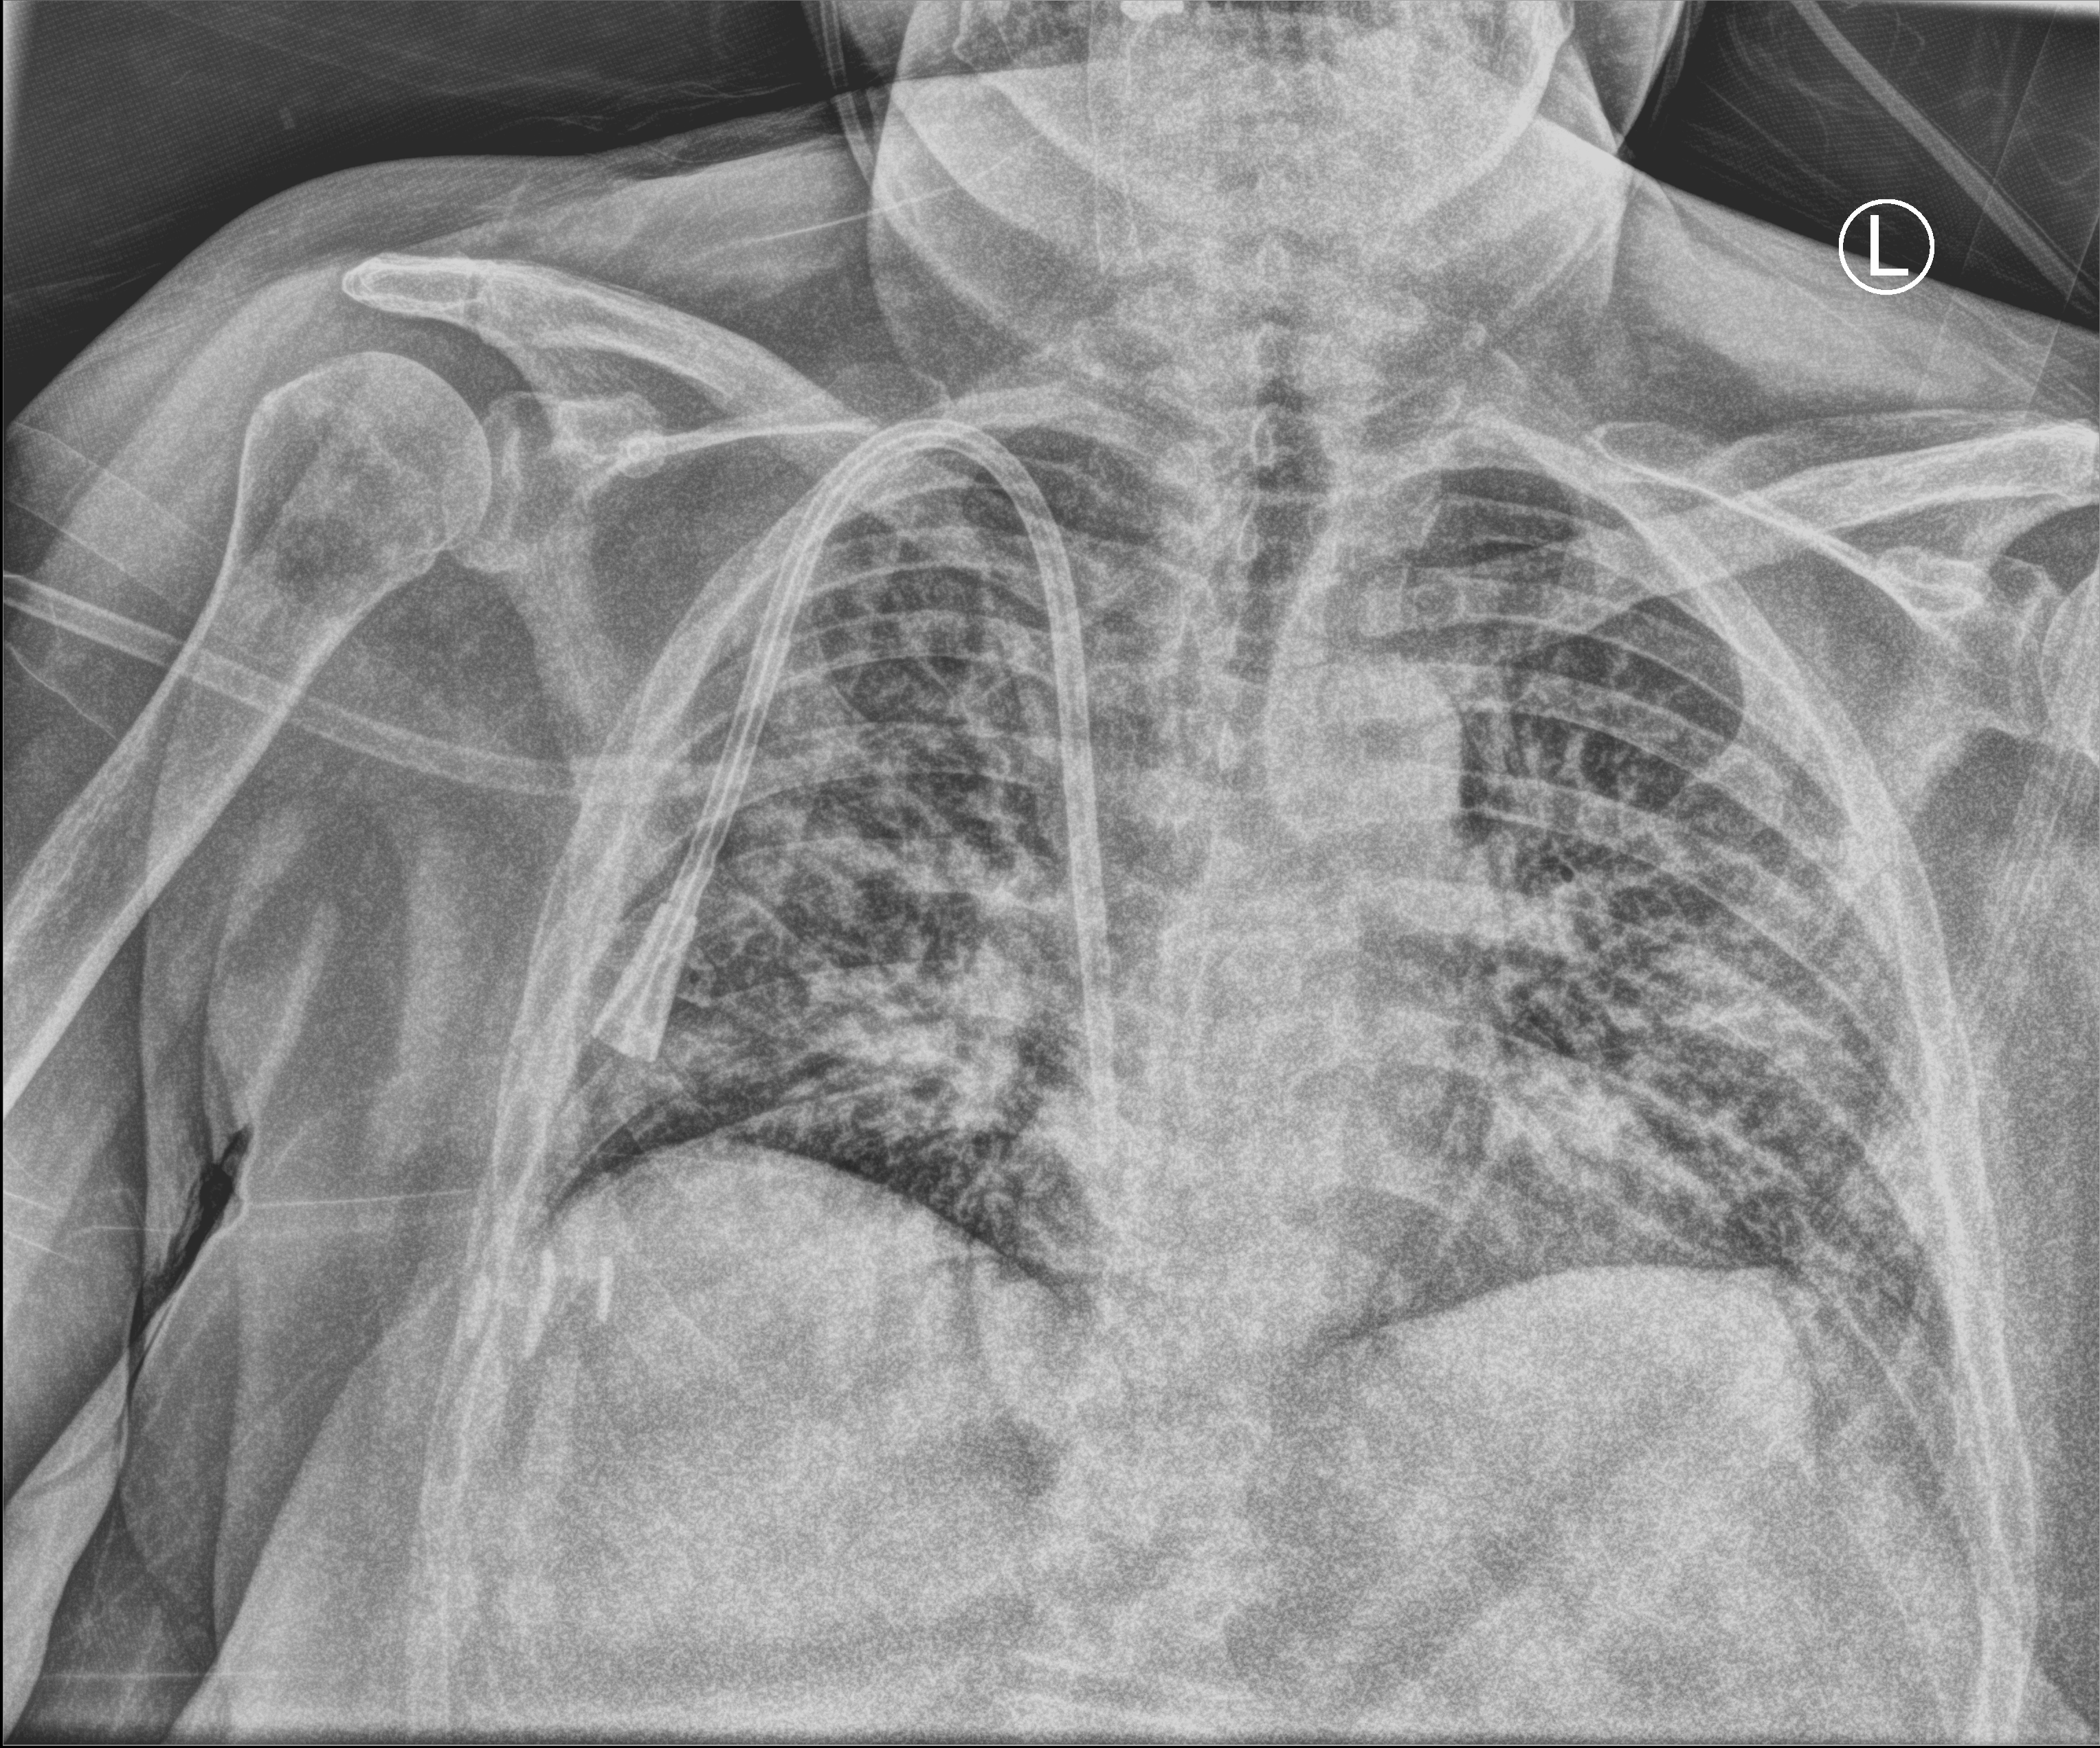
Chest X-ray (portable); anteroposterior (AP) projection. Female patient hospitalised with COVID-19, age 60–74 years.
From the hospital-stay record, not from the radiograph (when in the stay this image was taken is not recorded): admitted to intensive care during this hospital stay: no.